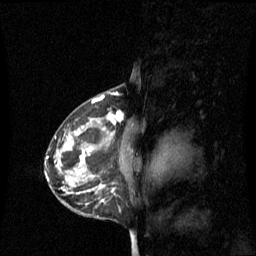
Breast MRI (dynamic contrast-enhanced), one sagittal slice; slice 40 of 60 in the series (ordered by position); dynamic contrast-enhanced series, image 2 of 3 at this slice position (ordered by acquisition); 1.5 T; TE 4.2 ms, TR 8.4 ms; 256 × 256 image matrix, field of view 240 × 240 mm. Female patient, age 42 years. Case-level facts recorded for this patient, not image findings: setting: breast cancer imaged before/during neoadjuvant chemotherapy; receptor status: HR-positive, HER2-negative.
Annotated regions visible in this slice (semi-automatic segmentation, software-assisted and operator-edited):
- analysis volume of interest (the breast-tissue region the enhancement analysis was run in; not a lesion): bounding box <68,112,137,201> (left, top, right, bottom; pixels)
- tumour enhancement mask (voxels above the 70 % enhancement threshold inside the analysis volume of interest): <80,112,123,201>